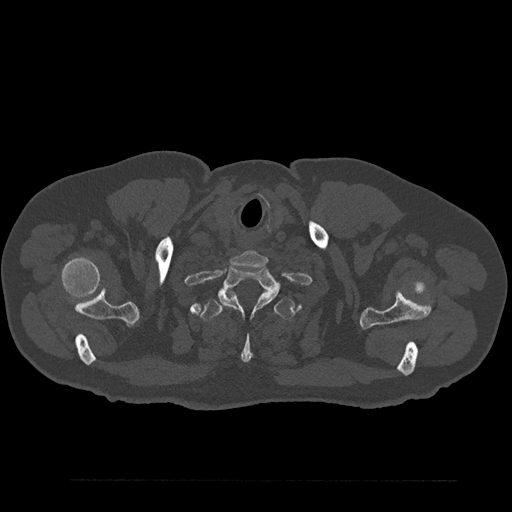
CT including the spine, one axial slice. Slice 744 of 797 in the series (ordered by position). Bone window (W 1800 / L 400 HU). 0.5 mm slice thickness. 512 × 512 image matrix. Male patient, age 61 years. Case-level facts recorded for this patient, not image findings: primary cancer: prostate.
Annotated regions visible in this slice (semi-automatically segmented with operator editing):
- T1 vertebra: box from (x=218, y=267) to (x=277, y=310) px
- T2 vertebra: (x=200, y=291)–(x=295, y=363)